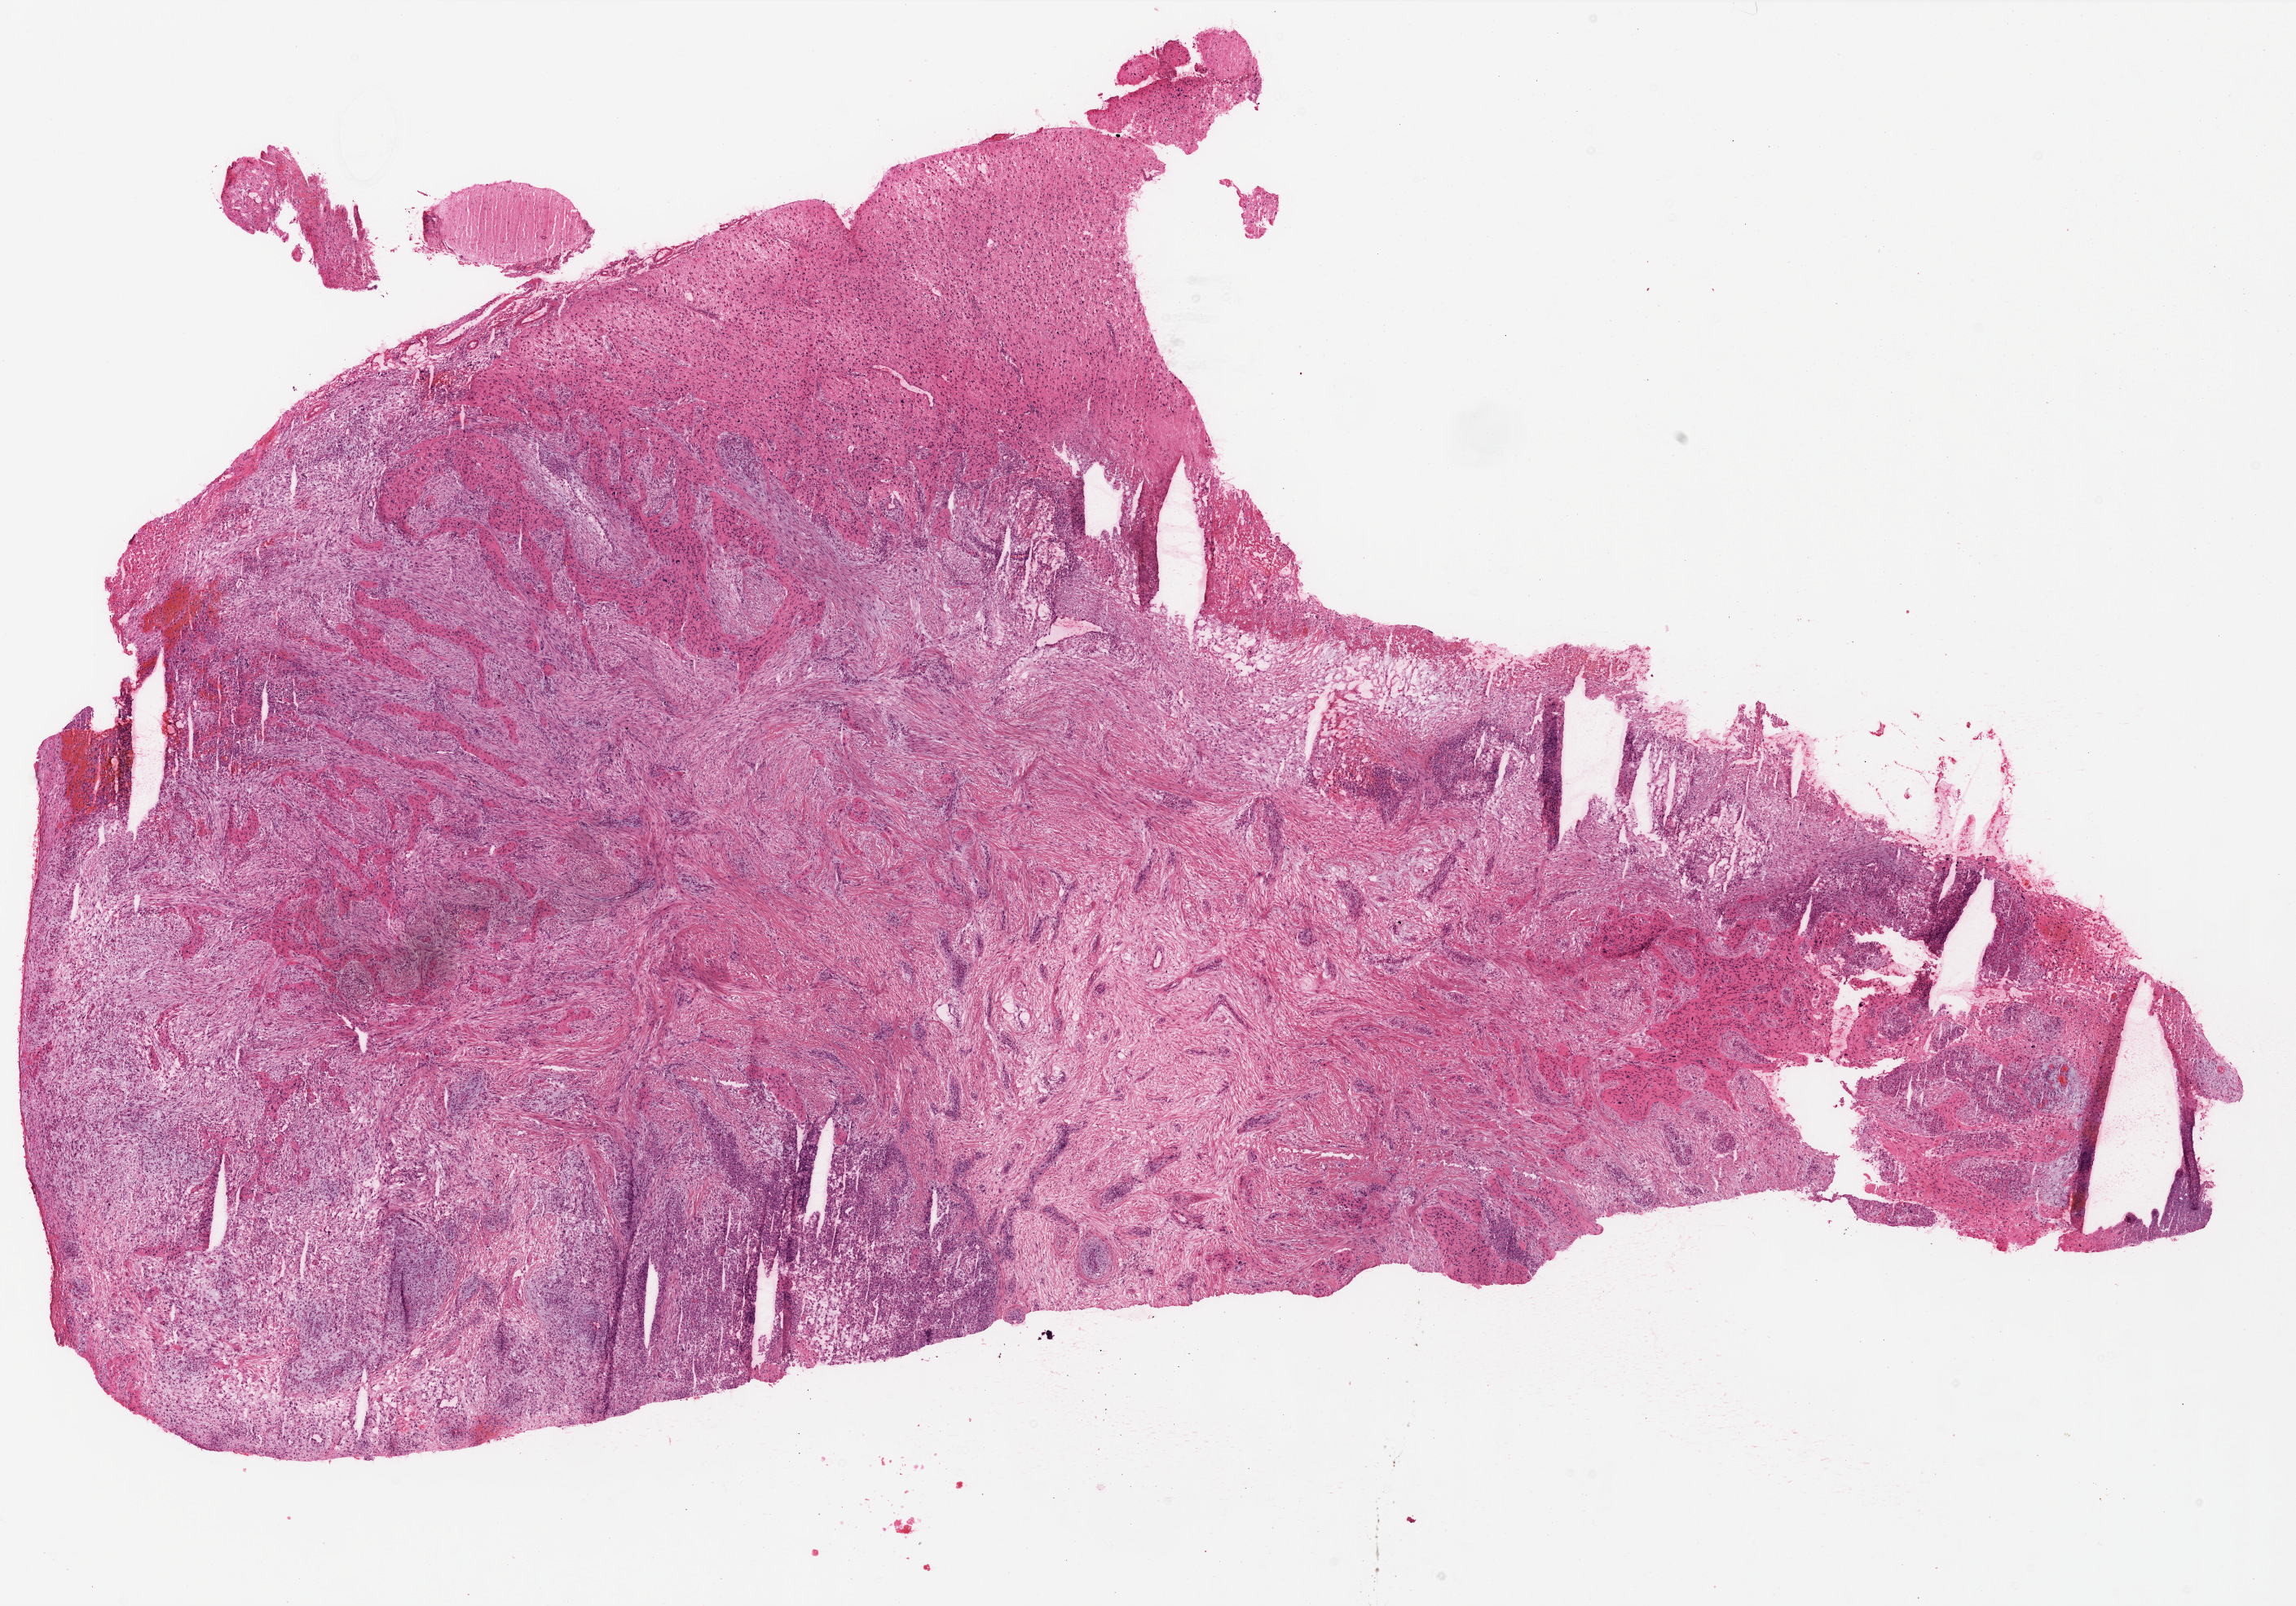
Digitized H&E-stained tissue section (whole slide), shown as a low-resolution overview of the whole scanned area (about 22.7 x 15.8 mm, from a 20x scan), frozen section, primary tumour sample from the brain. Male patient; age at initial diagnosis 59 years. Pathologist review of this section (percent, as recorded): tumour cells 95%, tumour nuclei 95%, normal cells 0%, stromal cells 5%, necrosis 0%.
- diagnosis: Glioblastoma